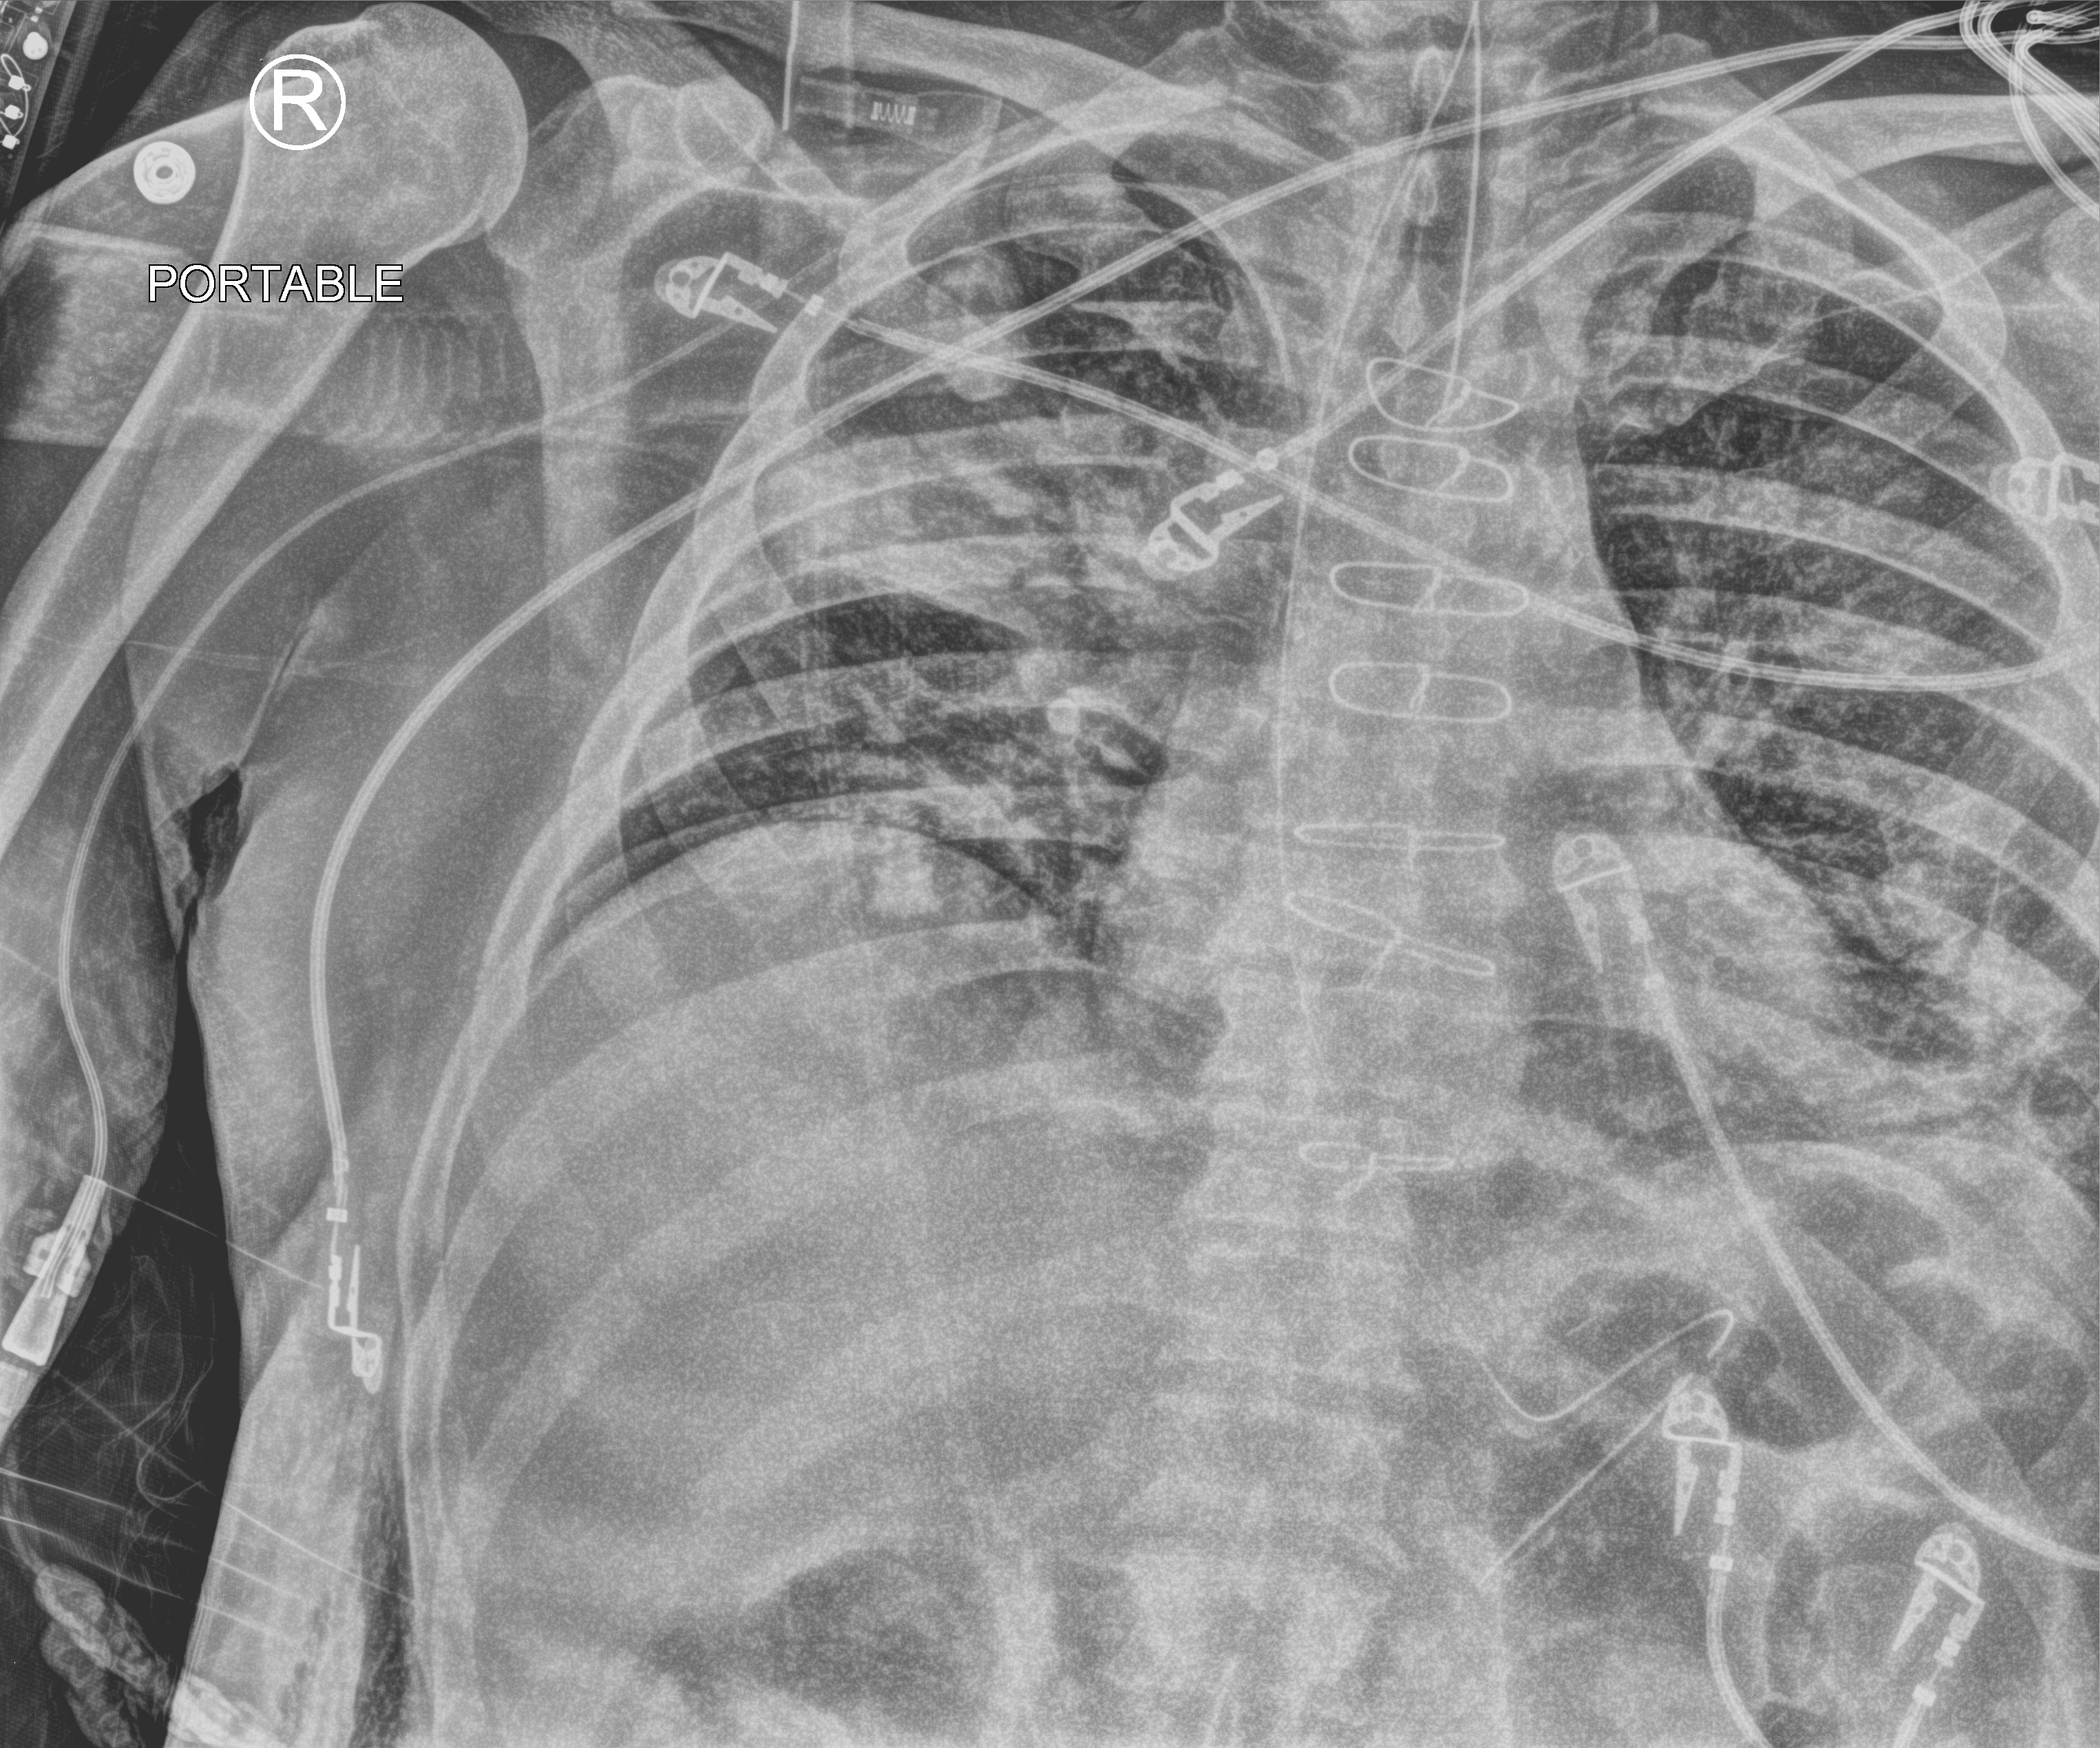
Portable chest radiograph. Male patient hospitalised with COVID-19, age 60–74 years.
From the hospital-stay record, not from the radiograph (when in the stay this image was taken is not recorded): mechanically ventilated during this hospital stay: yes.